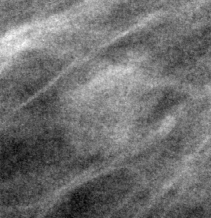
Region of interest cut from a scanned film mammogram (one marked finding); right breast; MLO view.
Mass, shape irregular, margins ill defined; BI-RADS assessment category 4; pathology result (as recorded, not read from the image): benign.